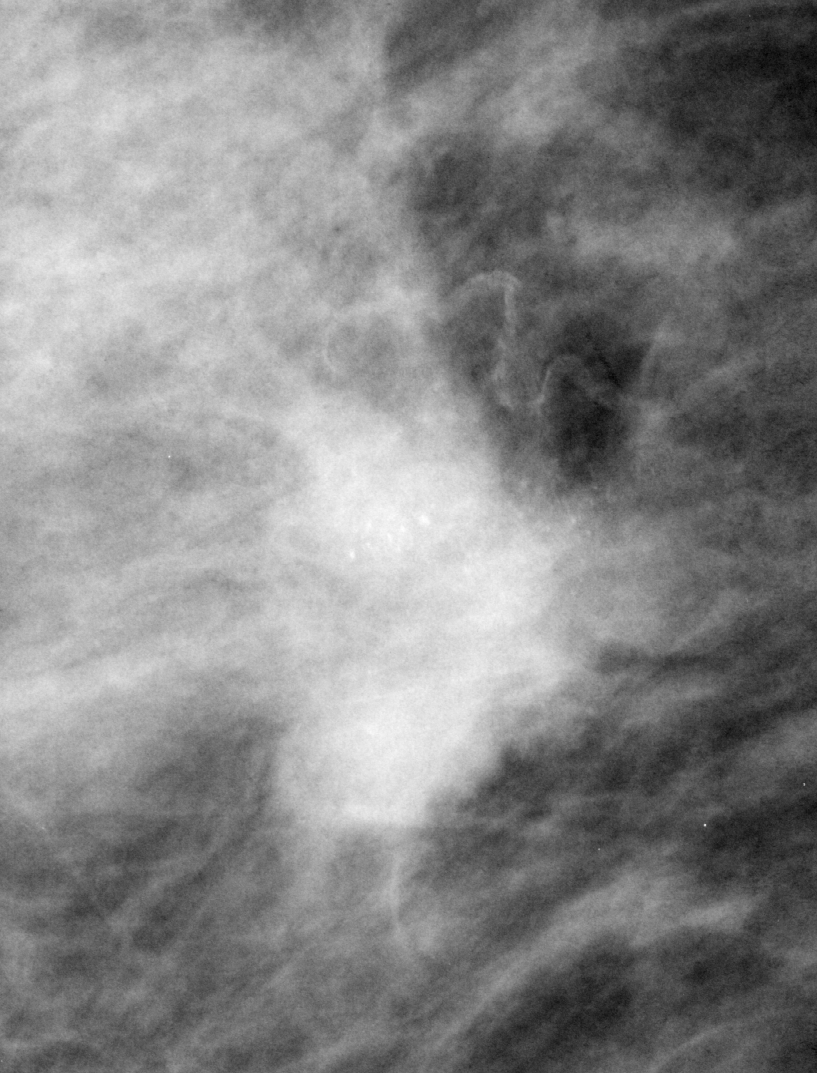
Crop from a digitized film mammogram around one marked abnormality, right breast, MLO view, BI-RADS breast density category 3 (scale 1–4).
- Marked abnormality: calcifications, morphology amorphous, distribution clustered; BI-RADS assessment category 5; subtlety rating 5 on a 1 (subtle) to 5 (obvious) scale; pathology result (as recorded, not read from the image): malignant.